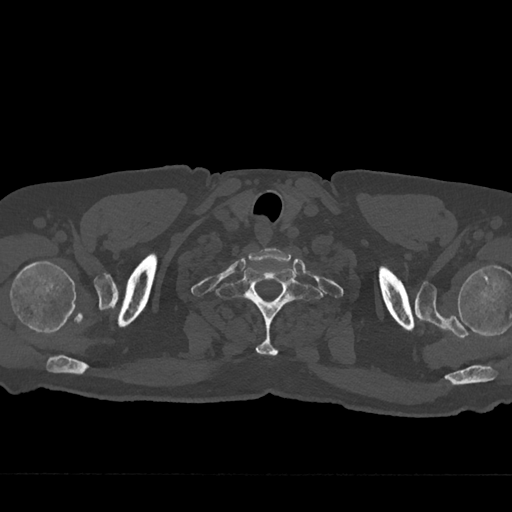
CT including the spine, one axial slice; position 664 of 797 along the scan axis; 120 kVp; bone window (W 1800 / L 400 HU); 0.5 mm slice thickness; 512 × 512 image matrix, field of view 377 × 377 mm. Patient: male, 75 years. From the clinical record (not read from this slice): primary cancer: renal; vertebrae with lytic lesions (as recorded): T4.
Annotated regions visible in this slice (semi-automatically segmented with operator editing):
- T1 vertebra: bounding box [x1, y1, x2, y2] px = [215, 267, 322, 356]
- T2 vertebra: [280, 293, 282, 295]